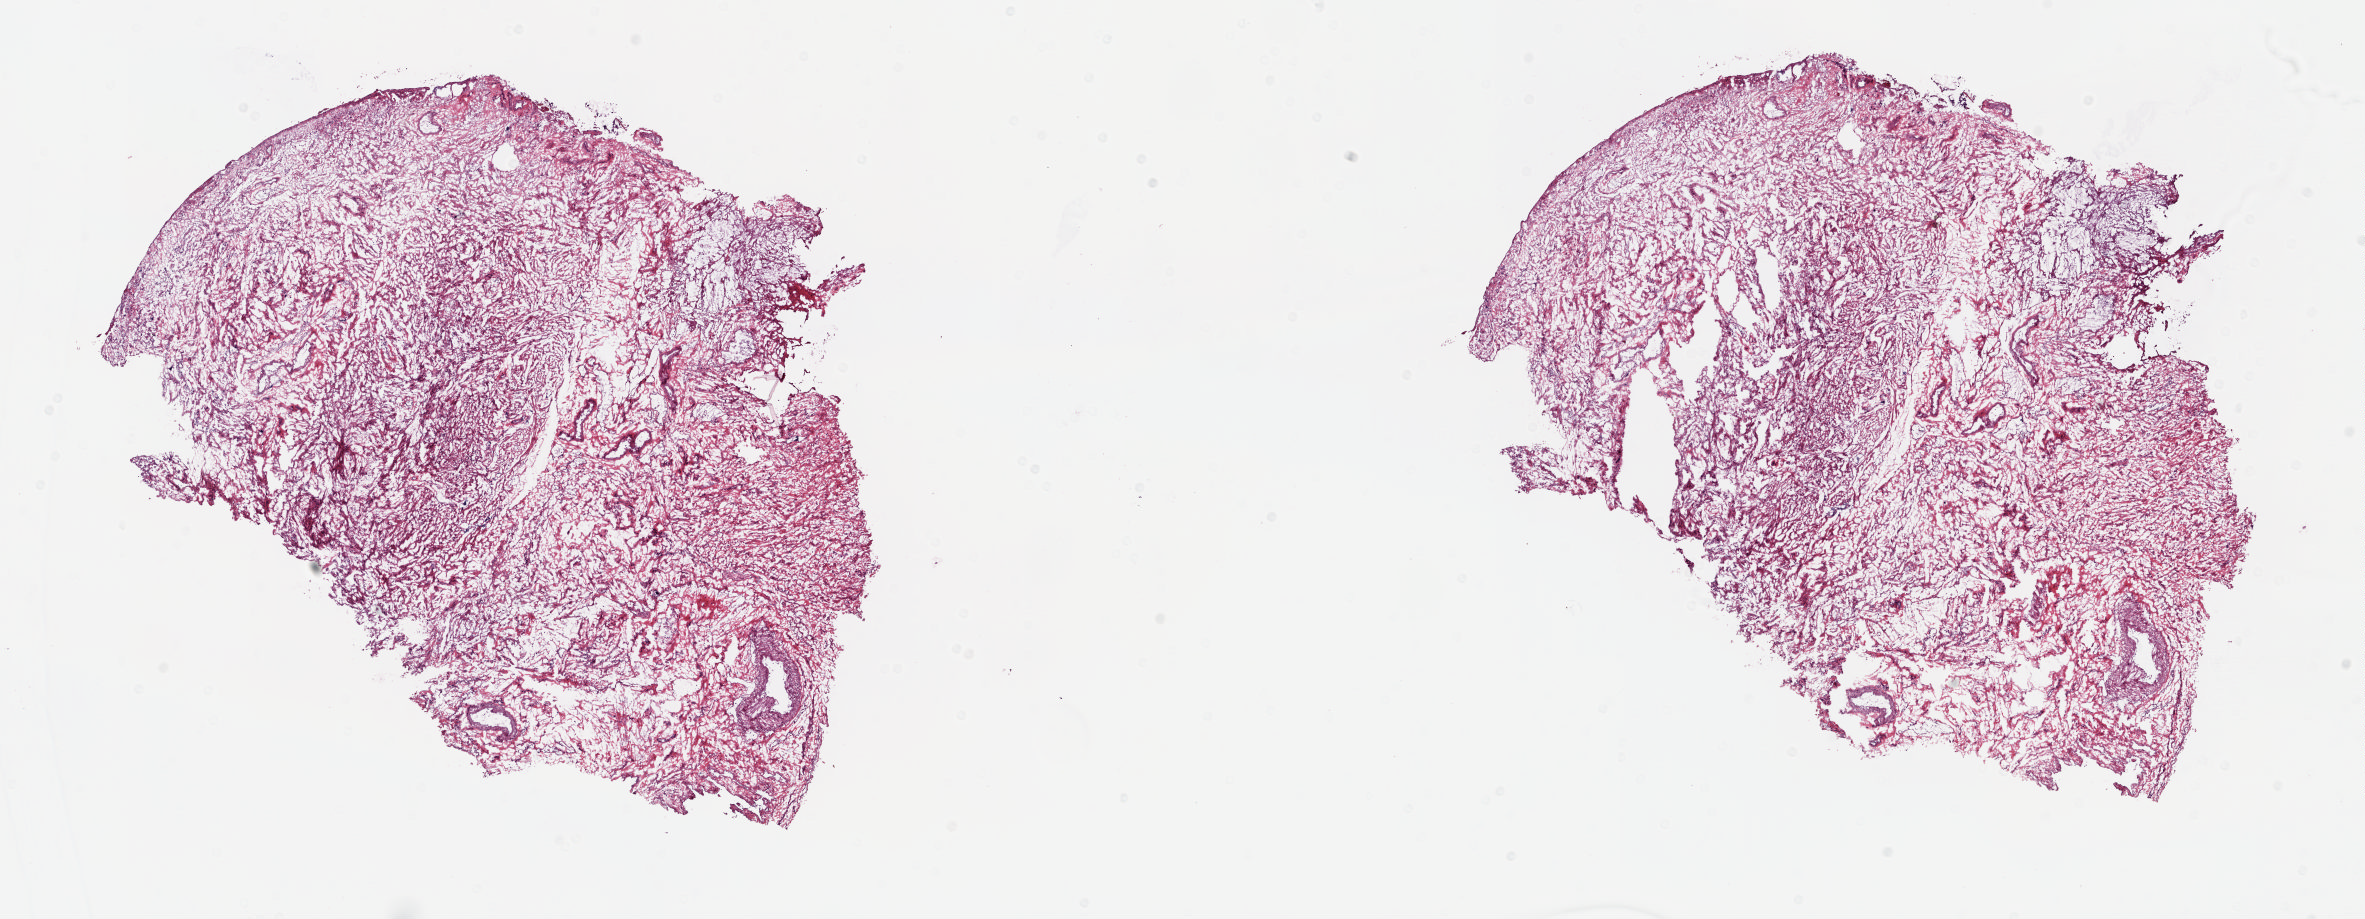
Digitized Hematoxylin and eosin (H&E) stained tissue section (whole slide), shown as a low-resolution overview of the whole scanned area (about 18.8 x 7.3 mm); frozen section; uterus, solid tissue normal (non-tumour tissue) sample. Patient: female, age at initial diagnosis 57 years. Slide review estimates, as recorded: tumour cells 0%, tumour nuclei 0%, normal cells 100%, stromal cells 0%, necrosis 0%. Inflammatory infiltration, as recorded: lymphocyte infiltration 40%, monocyte infiltration 20%, neutrophil infiltration 20%.
* this section: solid tissue normal sample (biorepository sample class)
* patient diagnosis: Serous cystadenocarcinoma, NOS (endometrium)